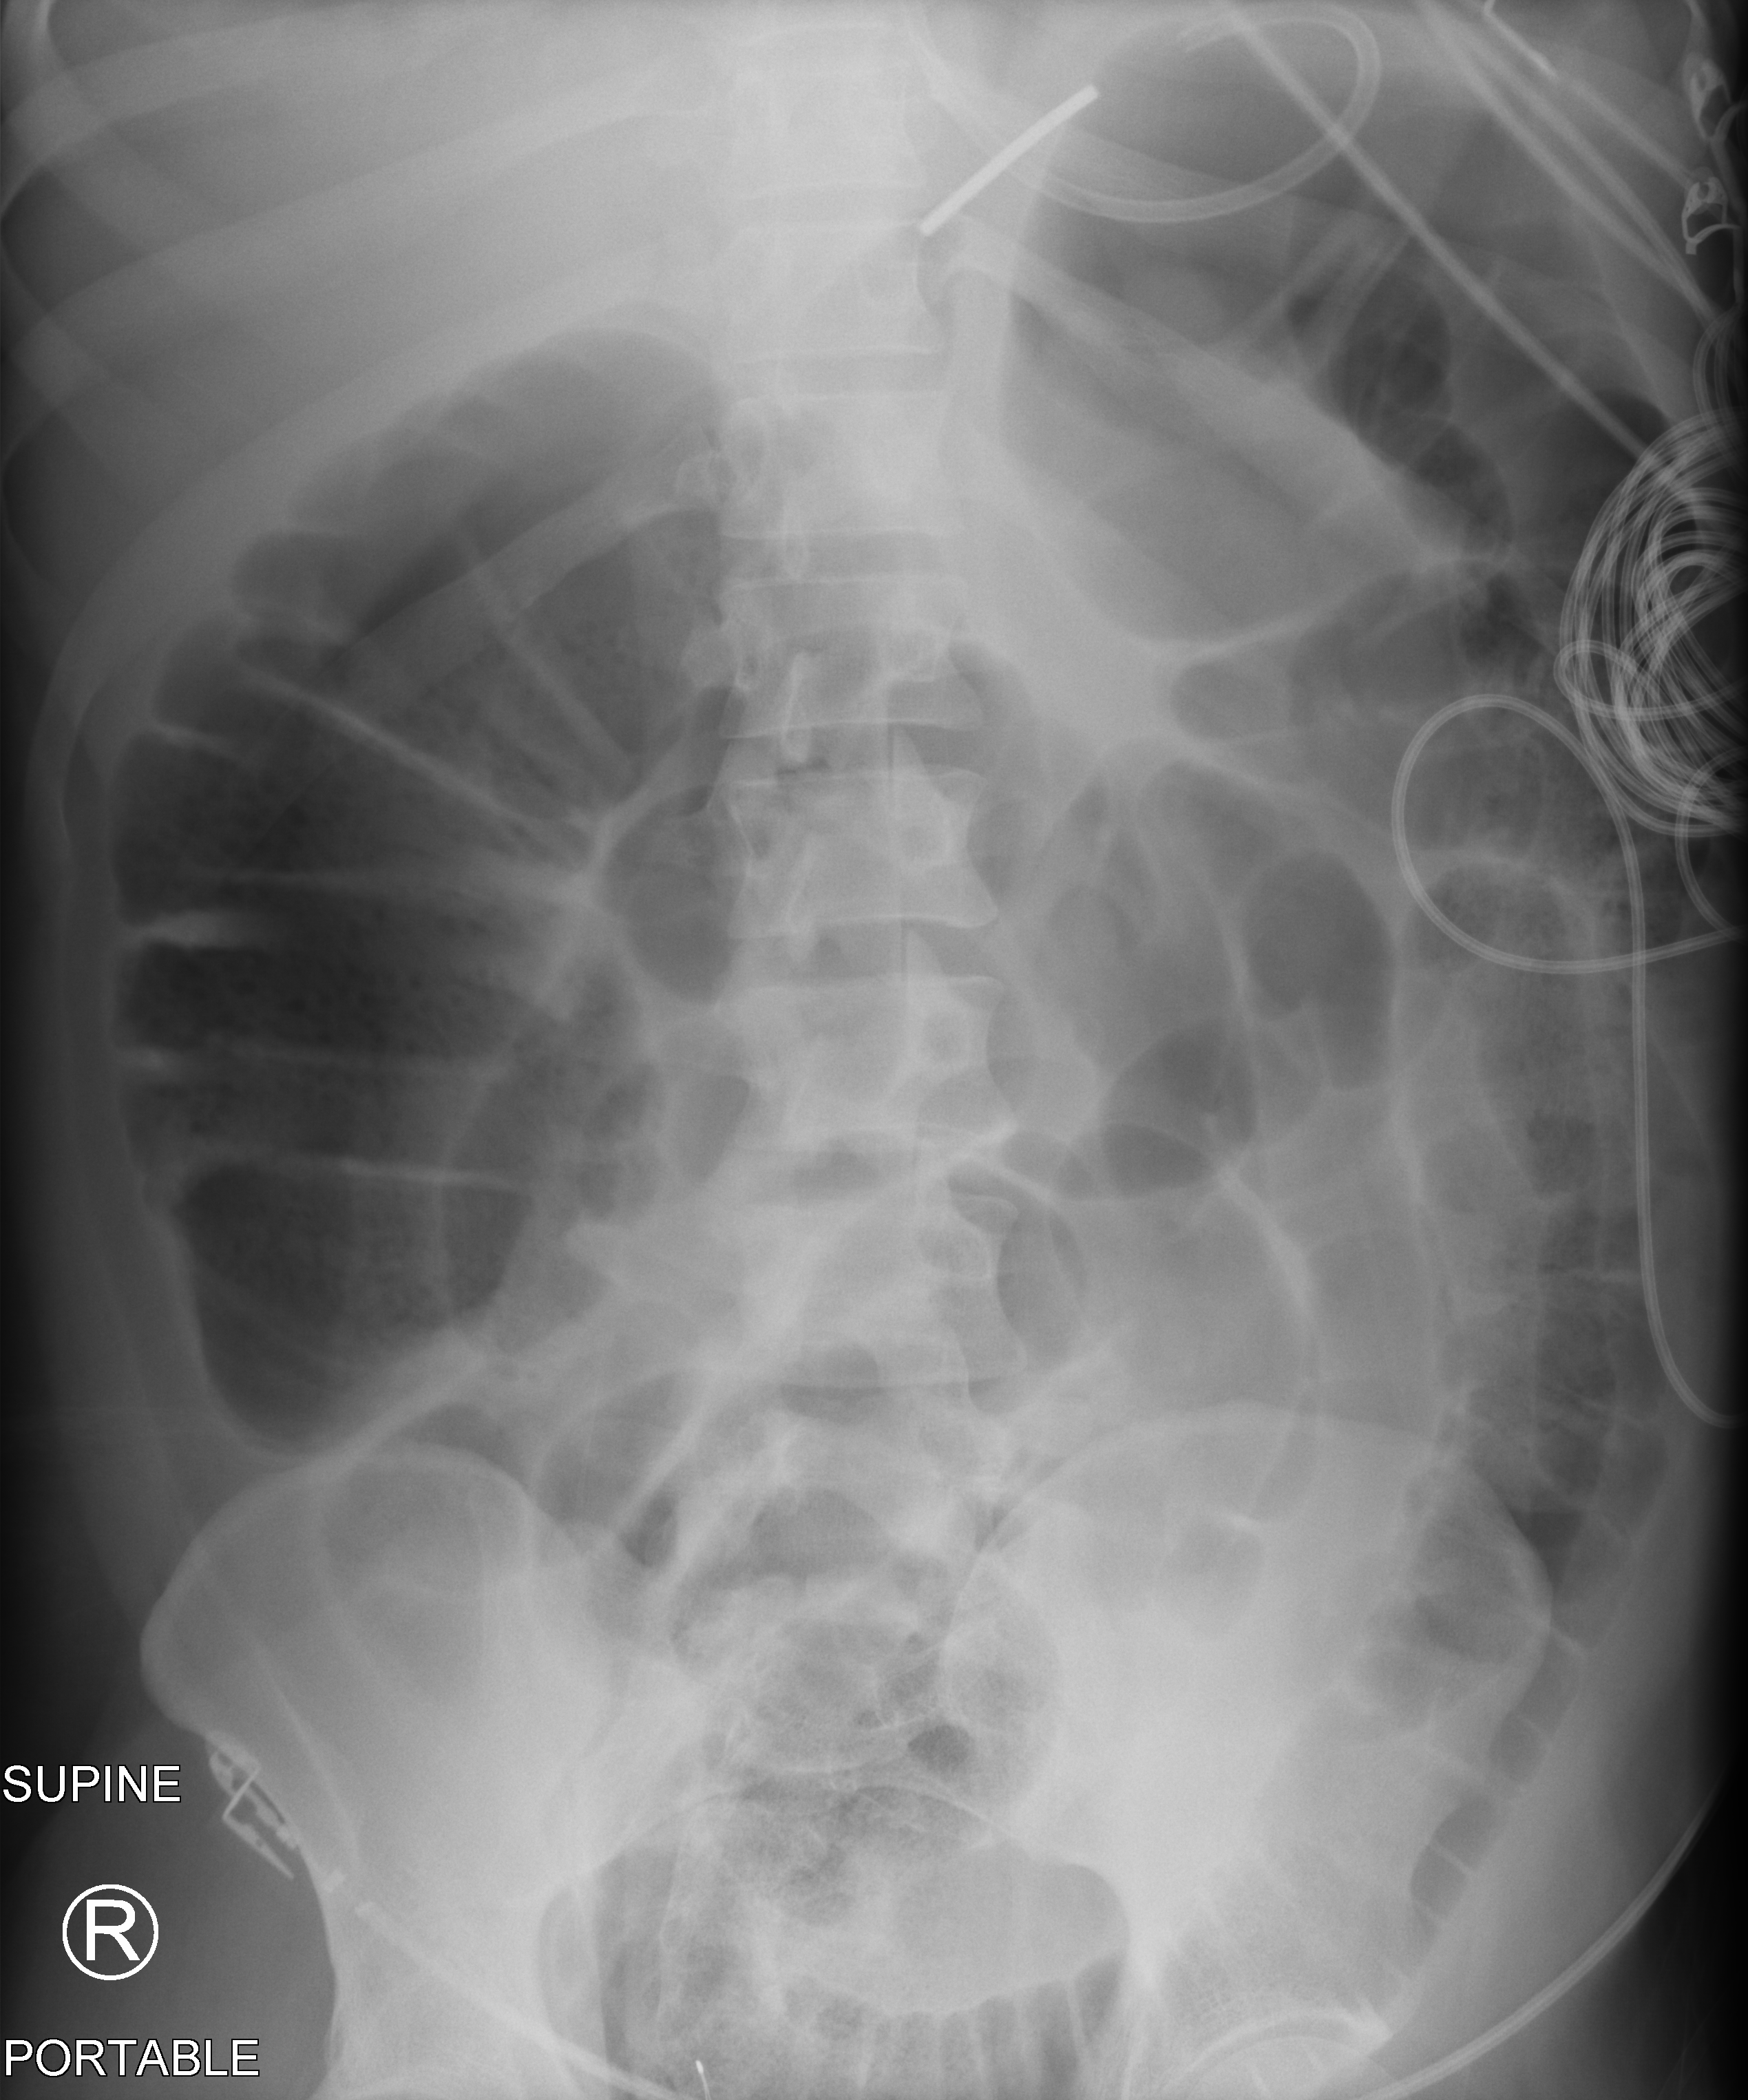
Bedside abdomen radiograph (computed radiography); anteroposterior (AP) projection. Patient hospitalised with COVID-19; male, aged 18–59 years.
From the hospital-stay record, not from the radiograph (when in the stay this image was taken is not recorded): mechanically ventilated during this hospital stay: yes.